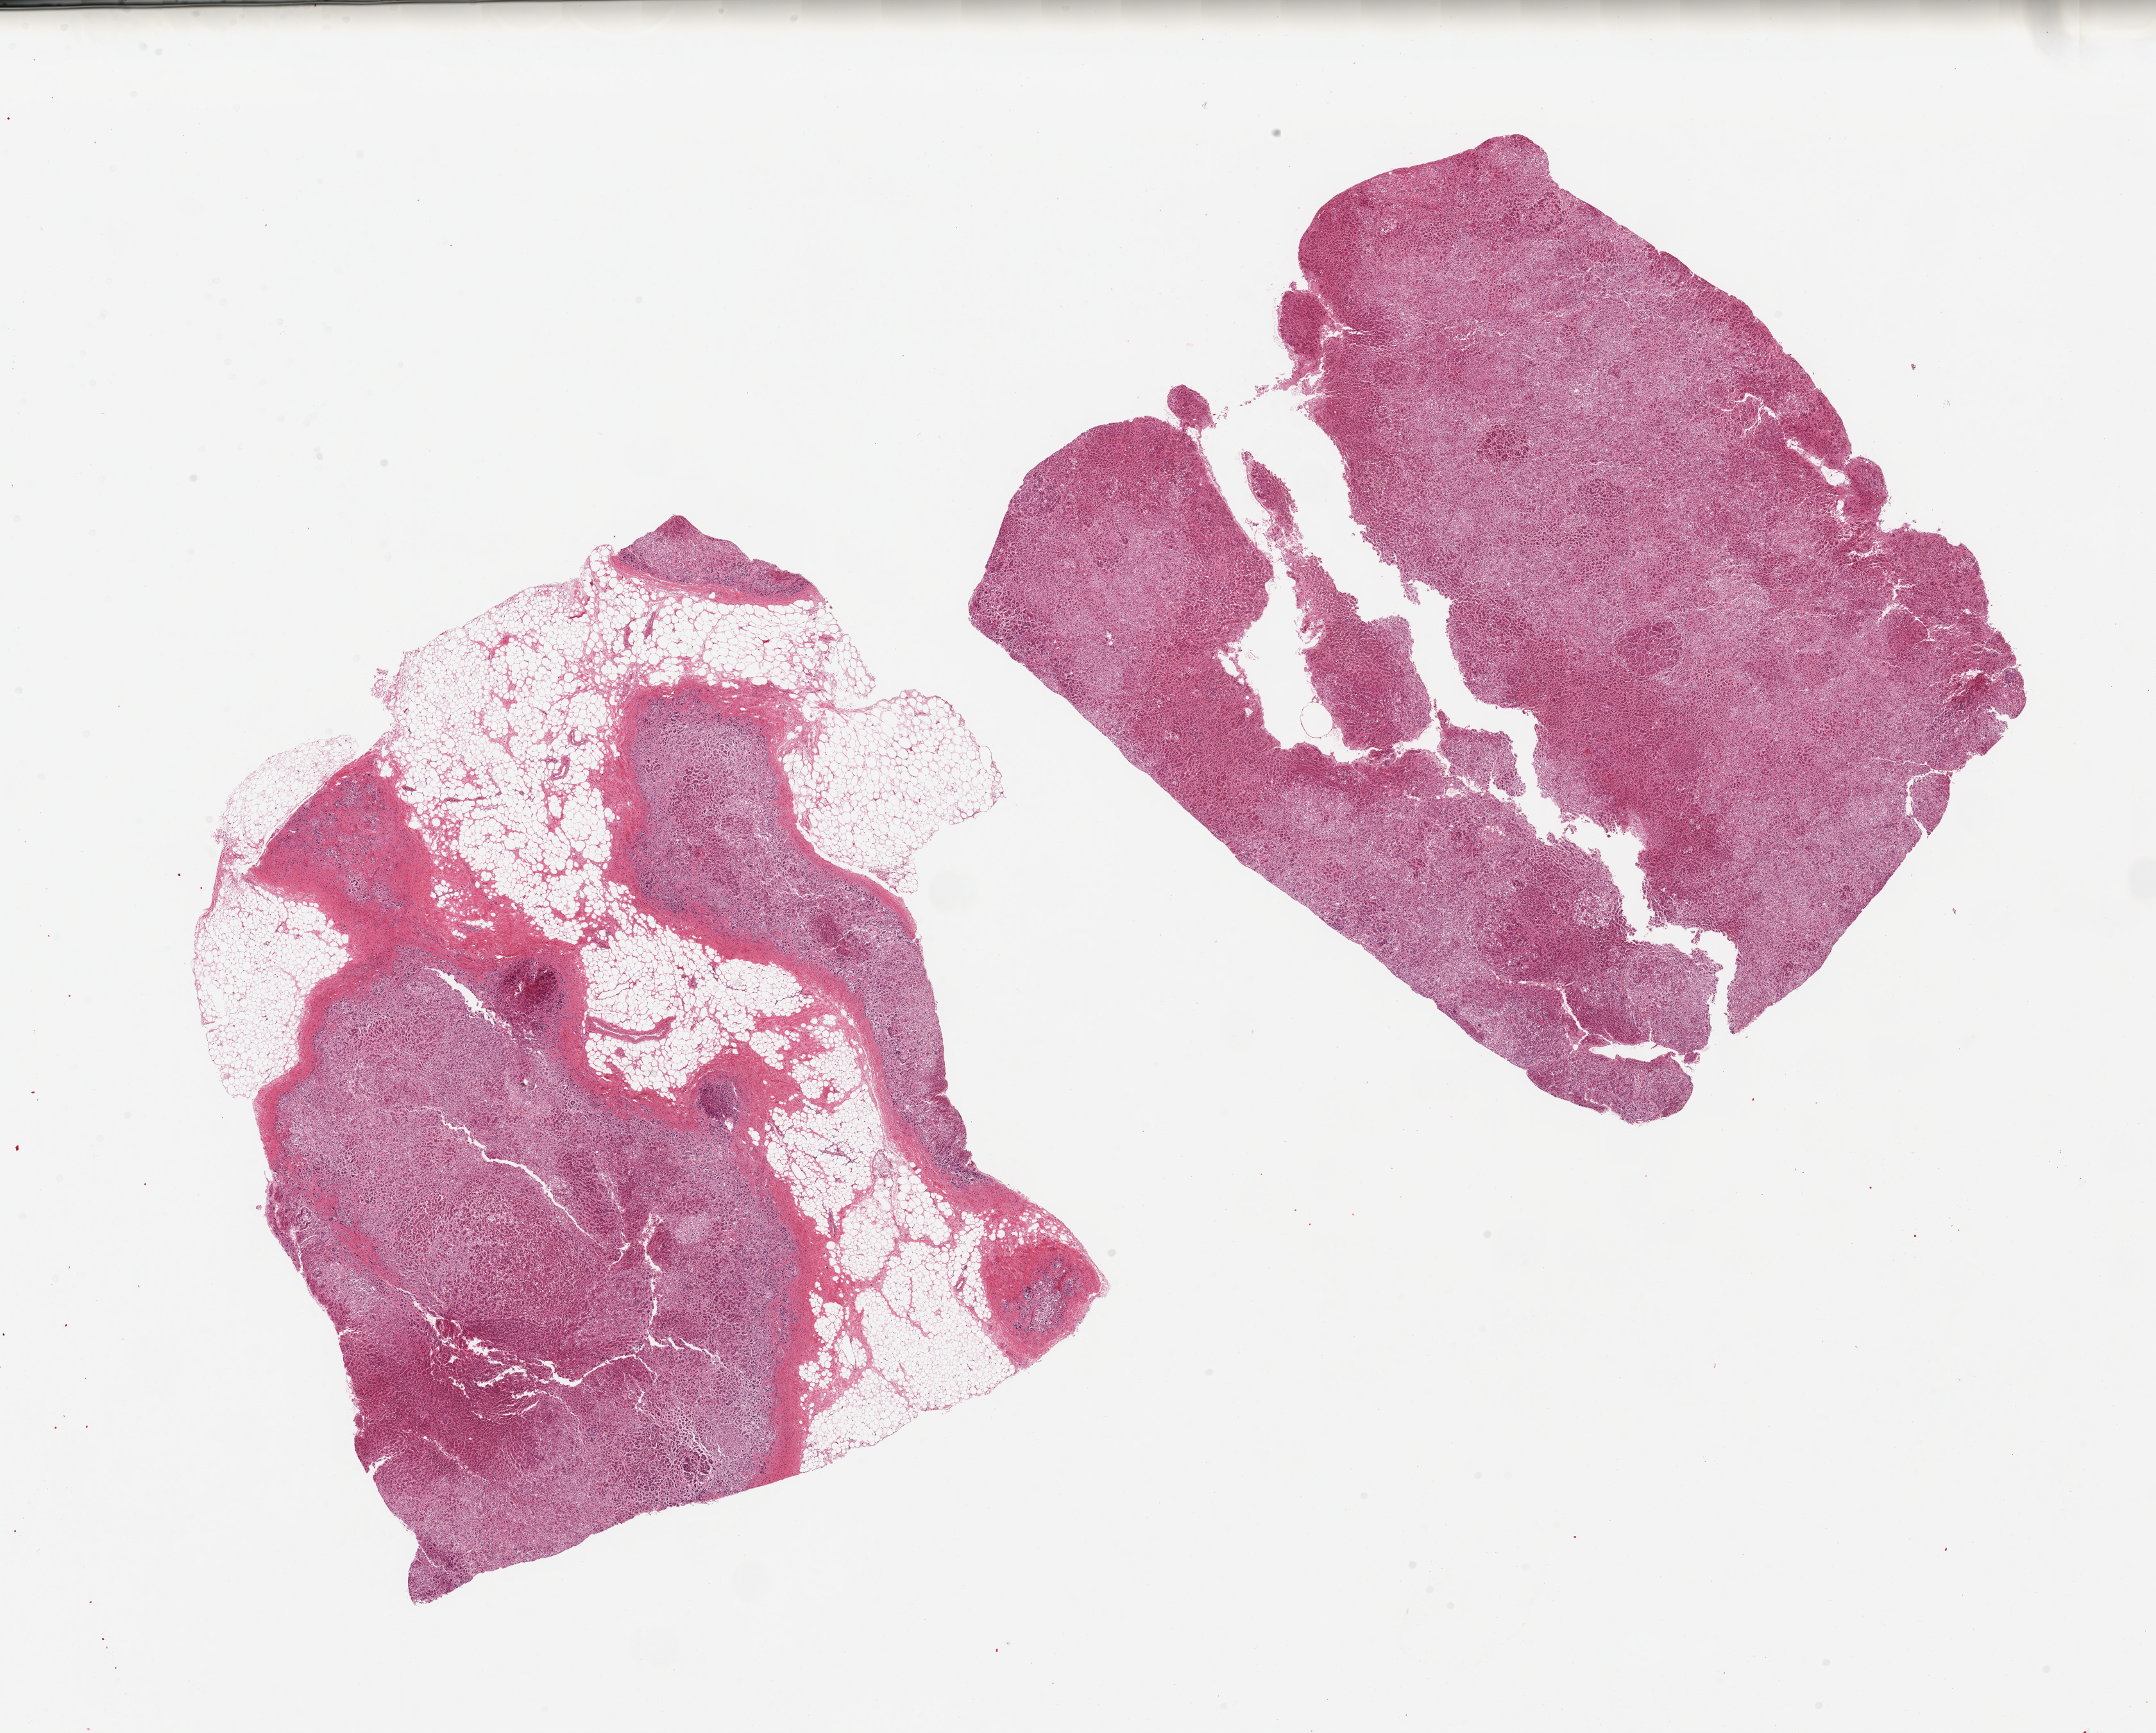
Hematoxylin and eosin (H&E) whole-slide image, shown as a low-resolution overview of the whole scanned area (about 26.6 x 21.4 mm, acquisition: 20x scan). PAXgene-fixed paraffin-embedded (PFPE) section. Sampled site (target tissue): adrenal gland. Tissue donor sample. Donor sex: male.
• review note (as recorded): 2 fragmented pieces; 1 with 40% fat, other fat free